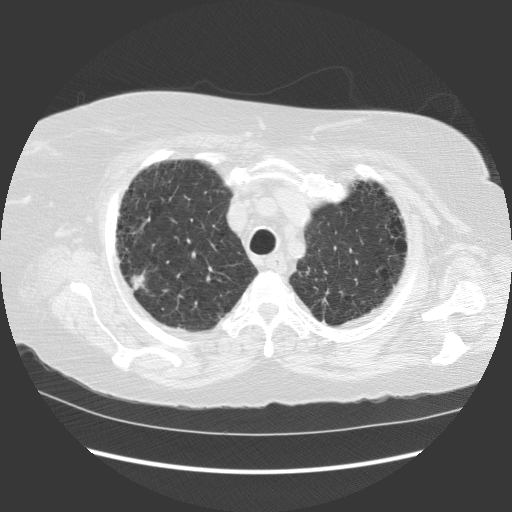
Low-dose screening chest CT, one axial slice. Position 99 of 121 along the scan axis. Reconstruction kernel STANDARD. 140 kVp. Lung window (W 1500 / L -600 HU). 2.5 mm slice thickness. 512 × 512 image matrix.
Annotated regions visible in this slice (outlined manually by an expert reader):
- lesion 1 (tumor, upper lobe of right lung): bounding box [x1, y1, x2, y2] px = [131, 274, 145, 290]